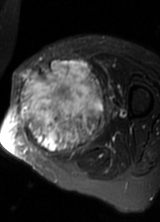
MRI of an extremity soft-tissue mass, one axial slice. Slice 34 of 69 in the series (ordered by position). T2-weighted fat-saturated. MR volume resampled by the dataset authors to the PET/CT grid (not the native acquisition matrix). 160 × 222 image matrix, field of view 156 × 217 mm. Female patient. From the clinical record (not read from this slice): histological type: pleomorphic leiomyosarcoma; grade: high; site of the primary tumour: left thigh.
Structures marked on this image (expert contour drawn on MRI and transferred to this co-registered scan by the dataset authors):
- gross tumour volume including surrounding oedema: bounding box (x1, y1, x2, y2) in pixels: (16, 59, 110, 158)
- gross tumour volume (mass): (16, 59, 106, 156)